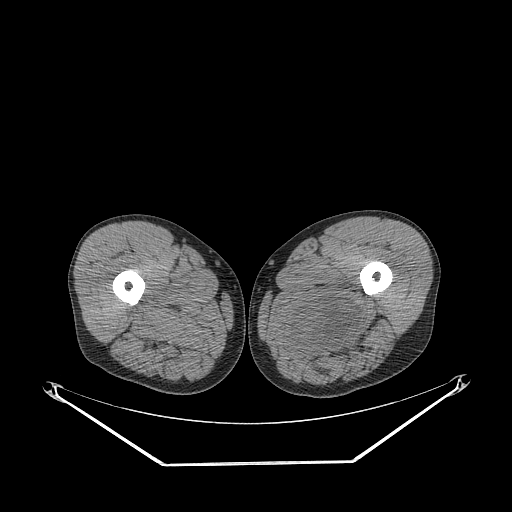
CT of an extremity soft-tissue mass (from a PET/CT study), one axial slice; slice 258 of 267 in the series (ordered by position); 140 kVp; soft-tissue window (W 400 / L 40 HU); 3.75 mm slice thickness; 512 × 512 image matrix. Male patient. Case-level facts recorded for this patient, not image findings: histological type: undifferentiated pleomorphic liposarcoma; grade: high; site of the primary tumour: left thigh.
Outlined on this slice (expert contour drawn on MRI and transferred to this co-registered scan by the dataset authors):
- gross tumour volume including surrounding oedema: bounding box [x1, y1, x2, y2] px = [285, 297, 364, 355]
- gross tumour volume (mass): [290, 299, 355, 353]